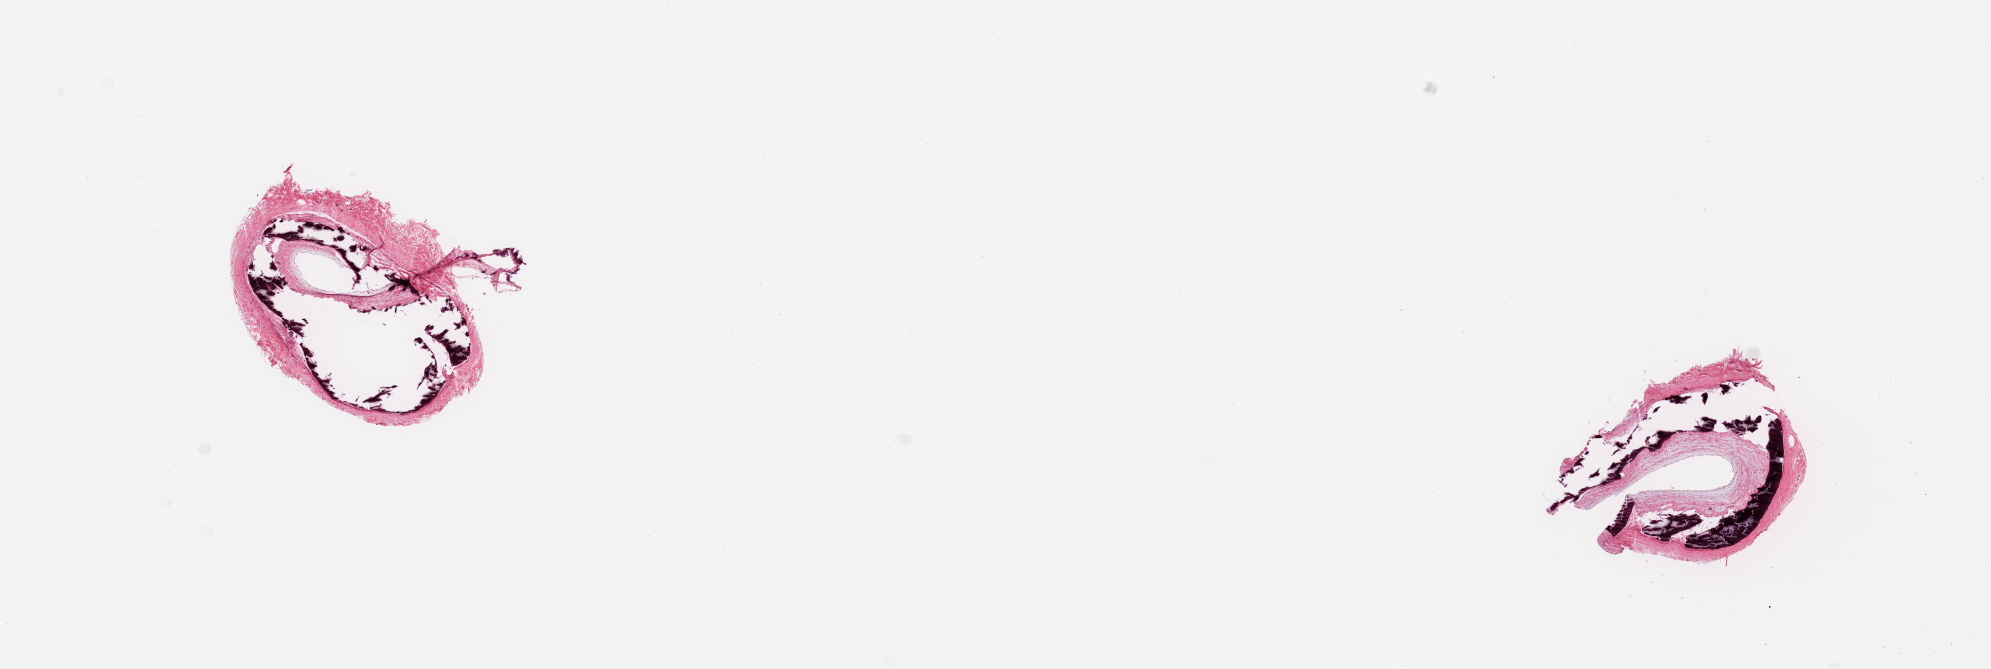
Digitized H&E-stained section, shown as a low-resolution overview of the whole scanned area (about 15.8 x 5.3 mm); PAXgene-fixed, paraffin-embedded tissue; sampled site (target tissue): tibial artery; donor tissue sample. Donor: female.
Pathologist's review note for this sample: 2 pieces; largely calcified with only small remnant of vascular tissues; of marginal value.